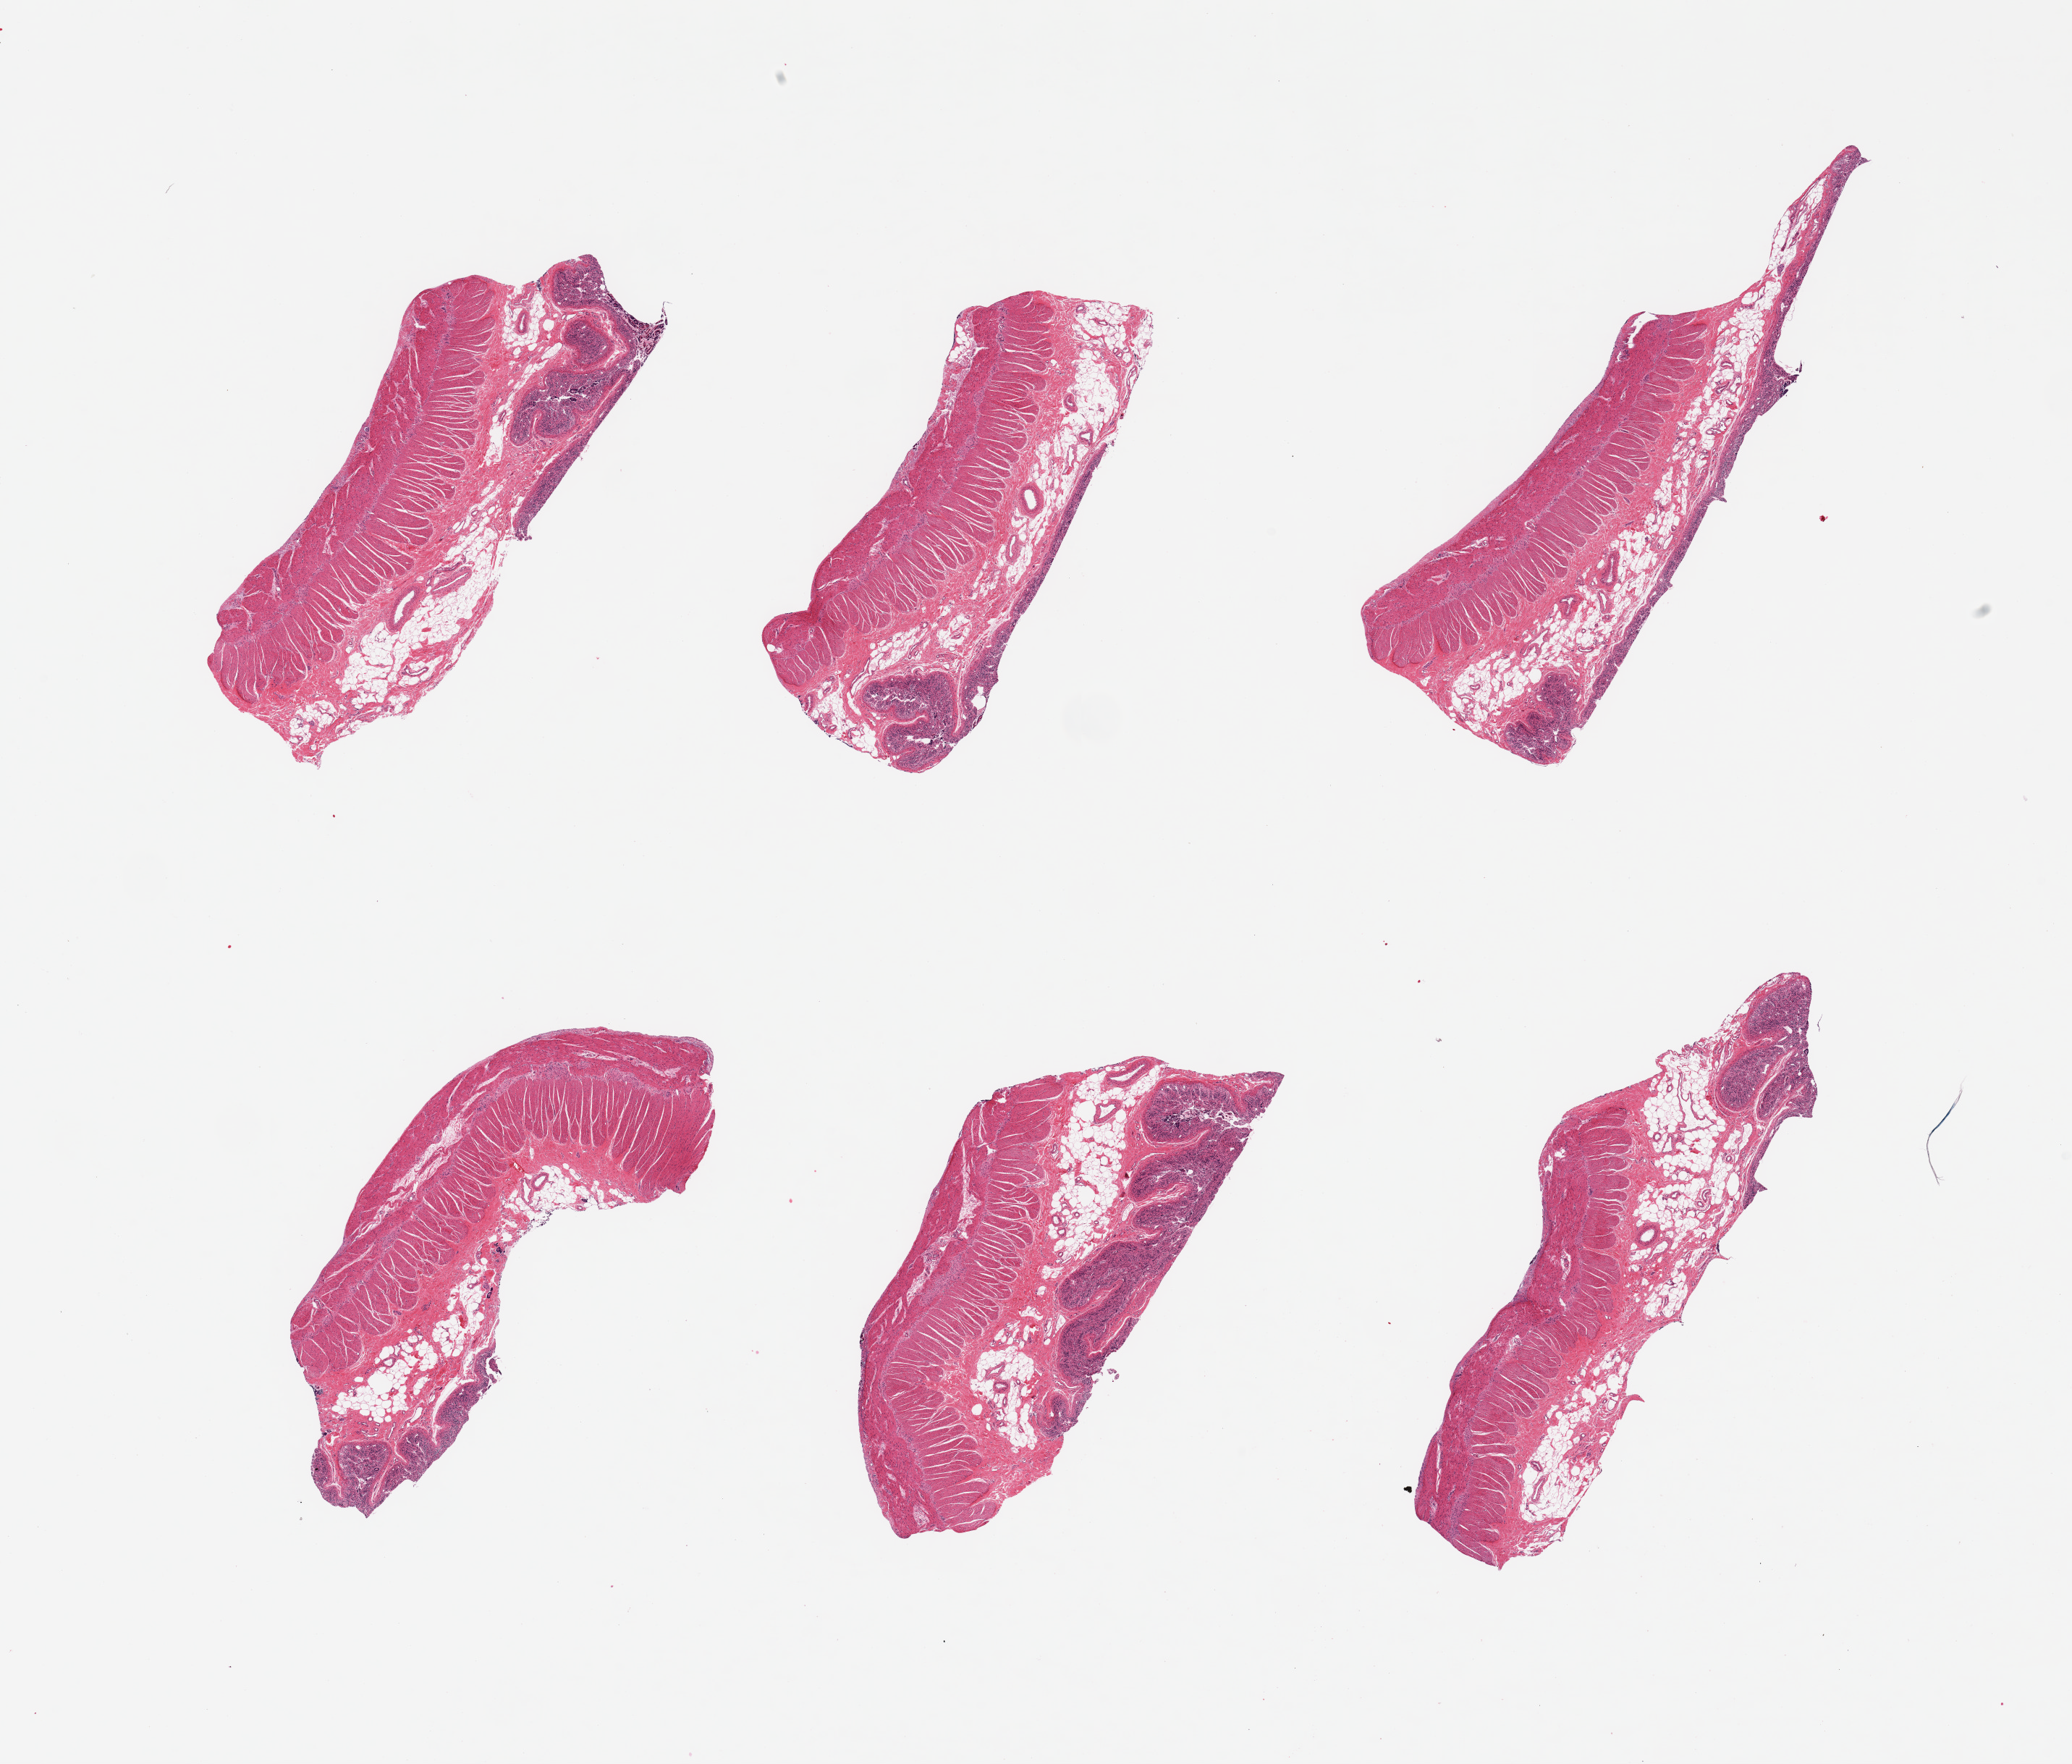
Whole-slide image, haematoxylin and eosin stain, a low-resolution overview of the entire scanned area, about 22.6 x 19.3 mm (acquisition: 20x scan), PAXgene-fixed paraffin-embedded (PFPE) section, sampled site (target tissue): ileum, donor tissue sample. Donor: male.
- pathologist's review note for this sample: 6 pieces, mucosa and muscularis; no target lymphoid aggregates in mucosa